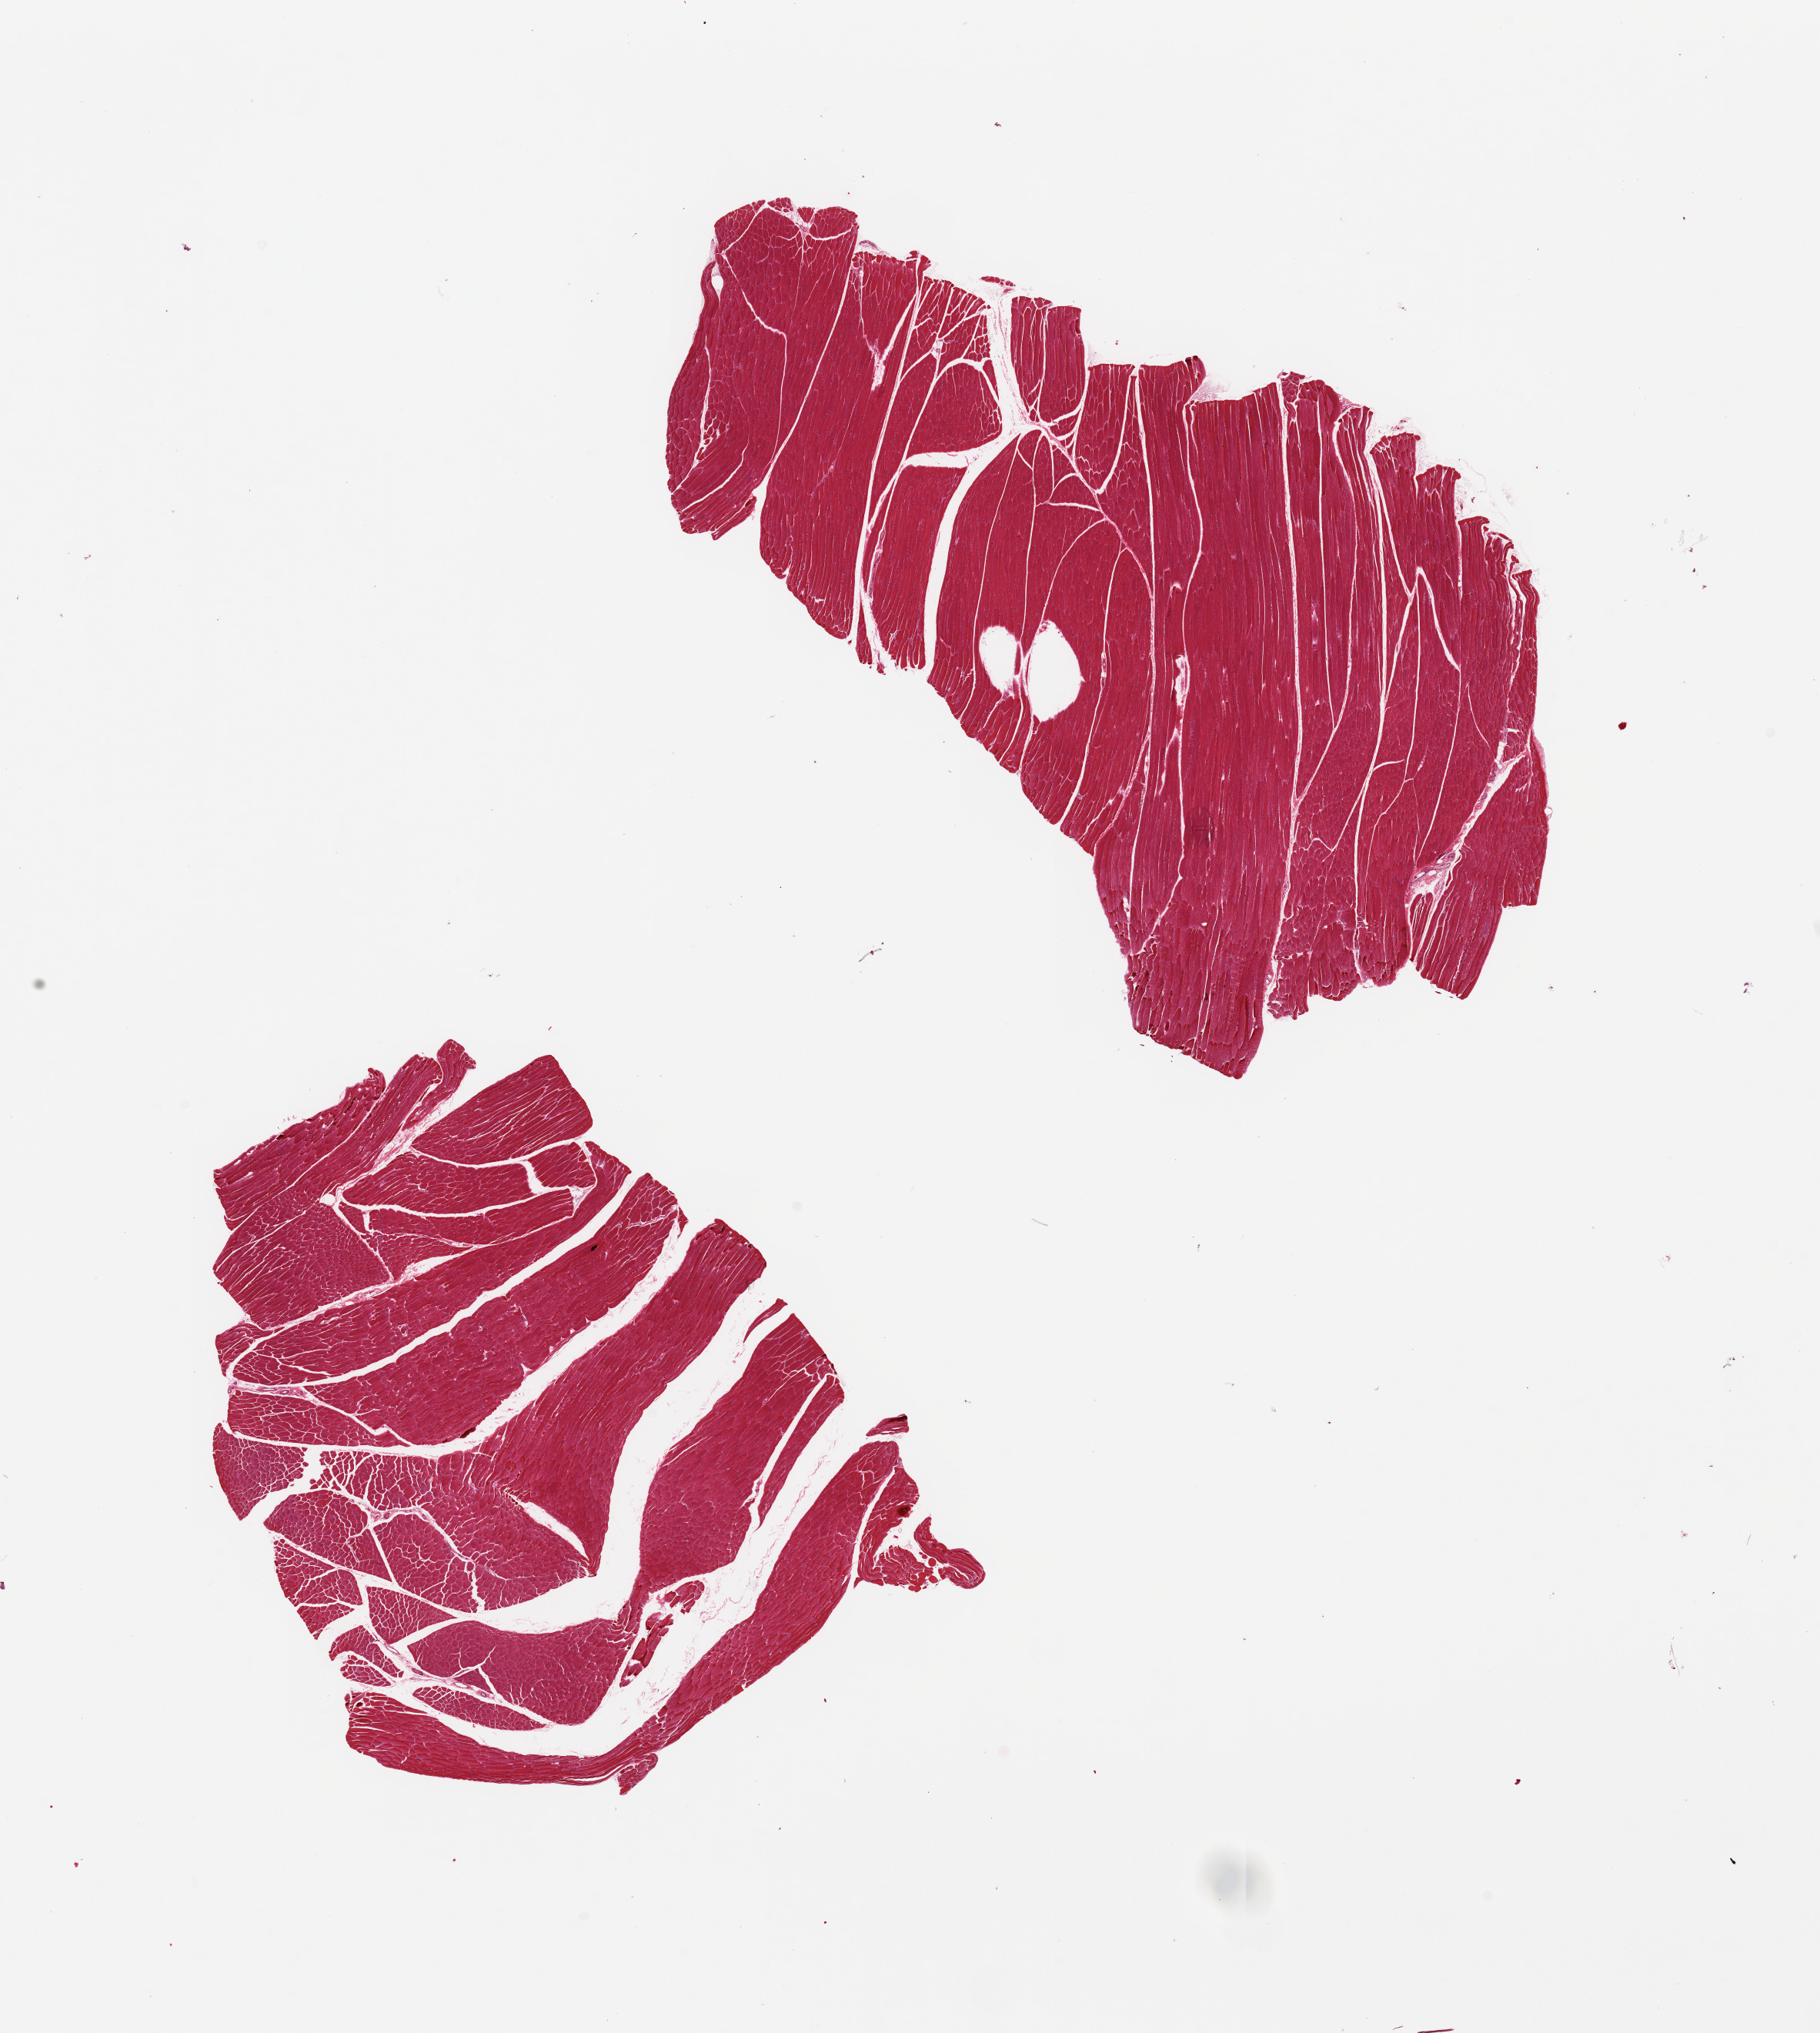
Whole-slide image, haematoxylin and eosin stain, a low-resolution overview of the entire scanned area, about 18.7 x 20.9 mm, PAXgene-fixed, paraffin-embedded tissue, section of skeletal muscle (target tissue), donor tissue sample. Donor sex: male.
• pathologist's review note for this sample: 2 pieces, minimal interstitial fat